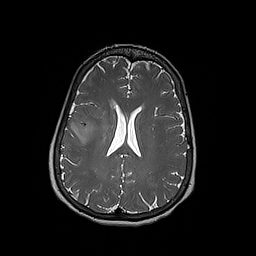
Brain MRI from a brain-tumour surgery series, one axial slice; slice 82 of 192 in the series (ordered by position); 1 mm slice thickness; 256 × 256 image matrix, field of view 250 × 250 mm. From the clinical record (not read from this slice): histopathology: Oligodendroglioma; WHO grade: 3; IDH mutation: yes.
Outlined on this slice (outlined manually by an expert reader):
- tumour: box from (x=73, y=116) to (x=95, y=138) px